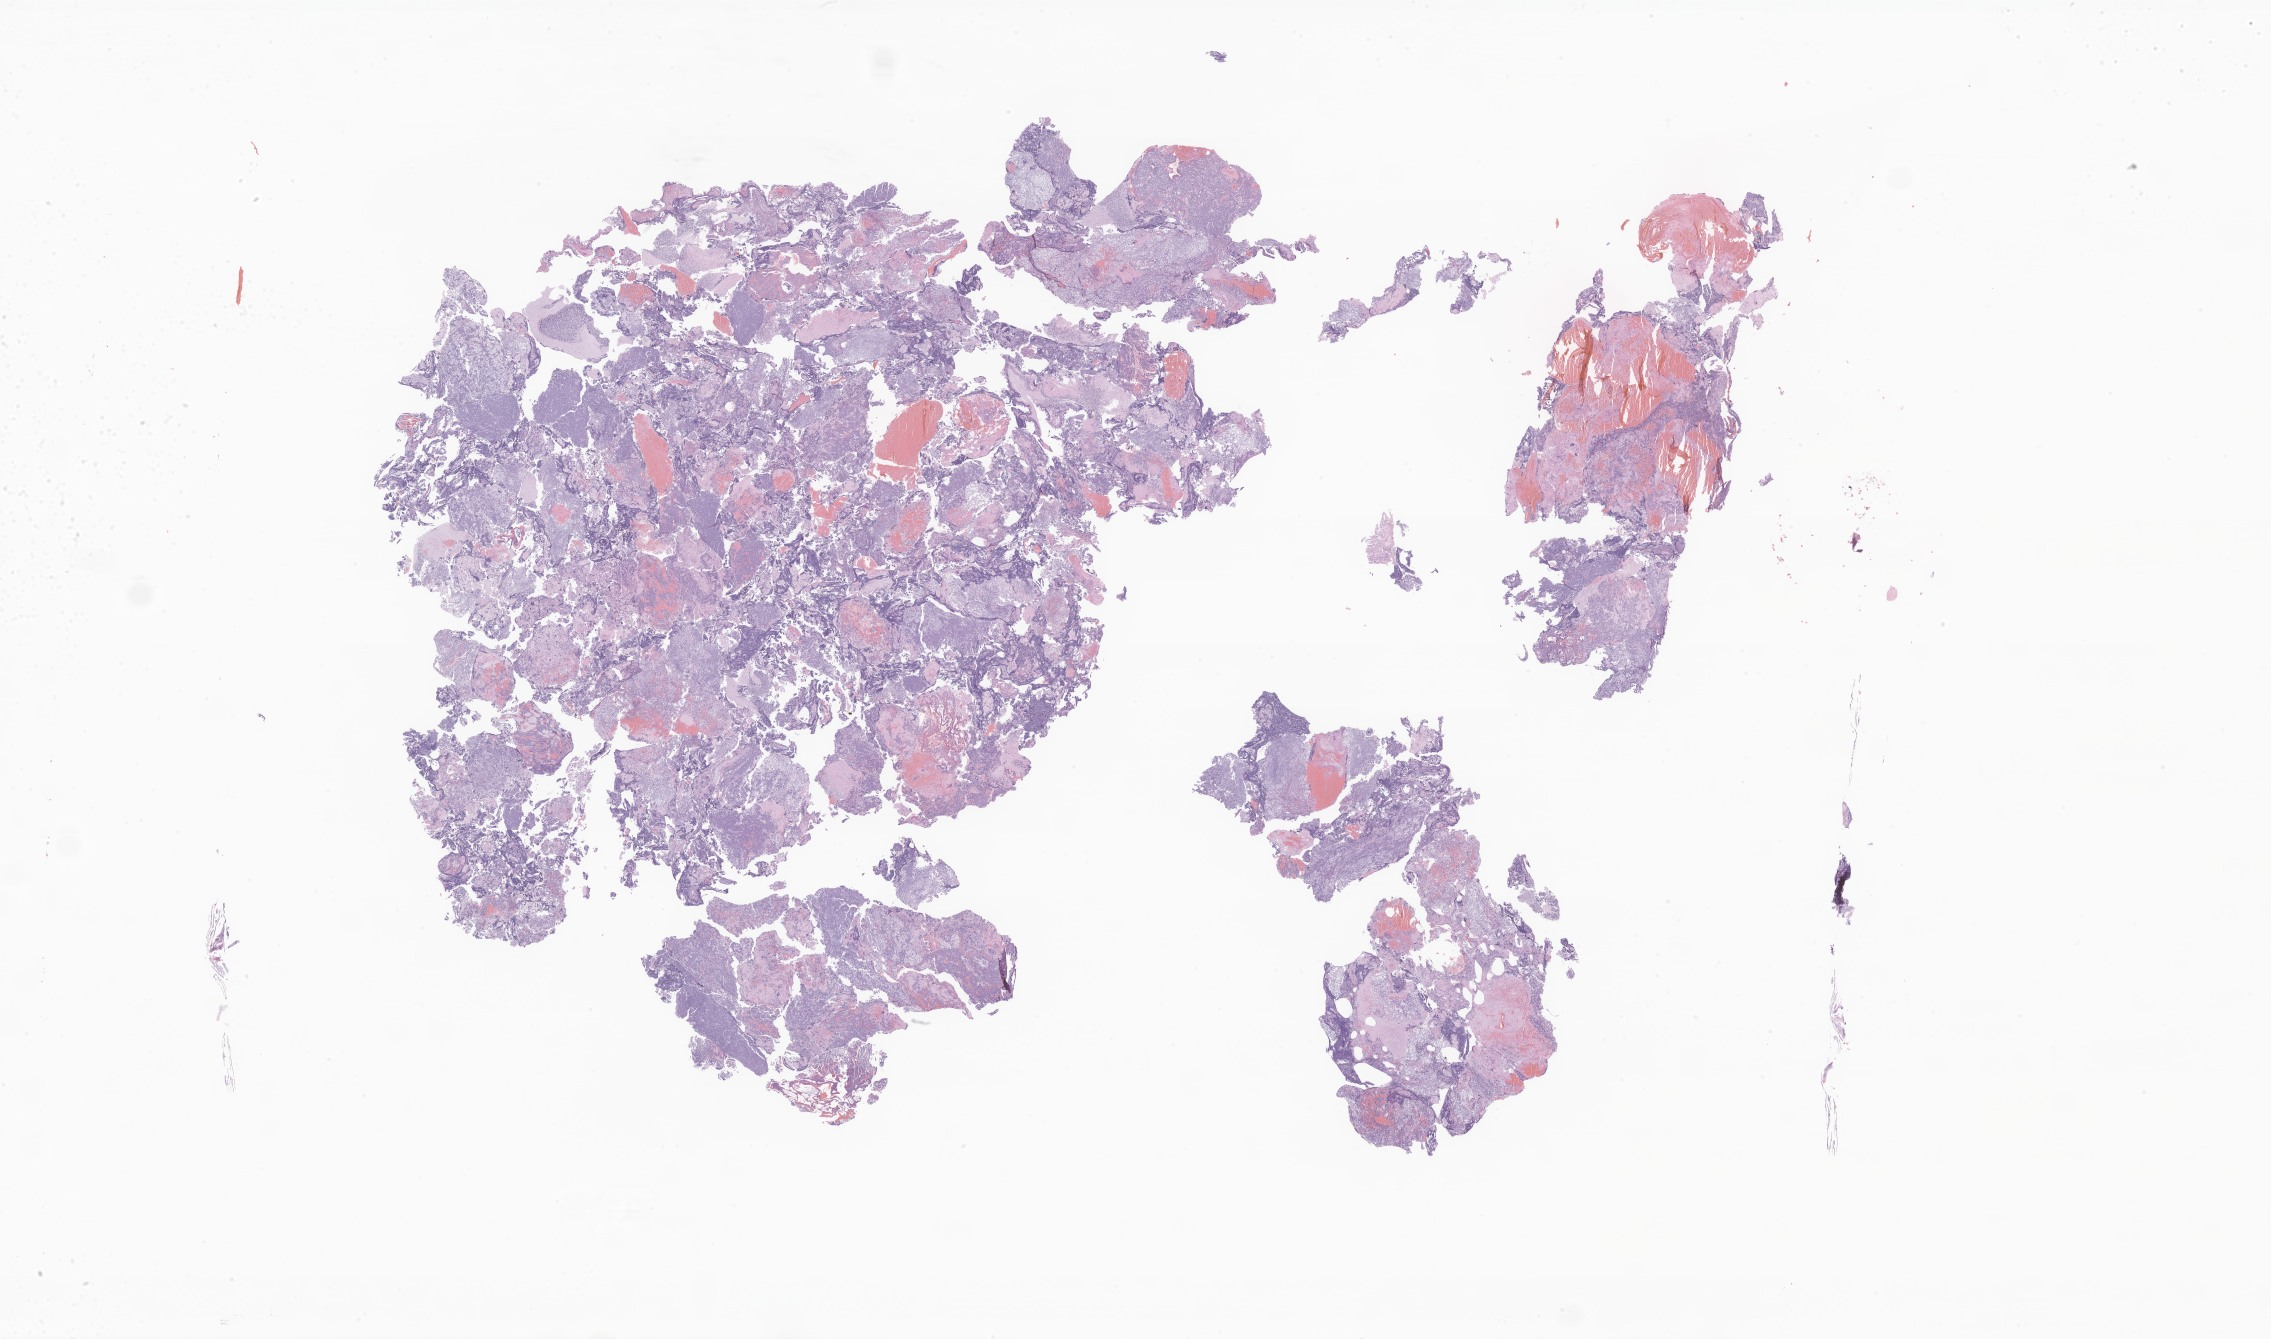
Whole-slide image, haematoxylin and eosin stain of tumor tissue from the brain, low-resolution overview of the scanned area, about 38.3 x 22.6 mm, FFPE section. Female patient, age 138 months (11 years 6 months).
Diagnosis (ICD-O-3 morphology term): Medulloblastoma, NOS.